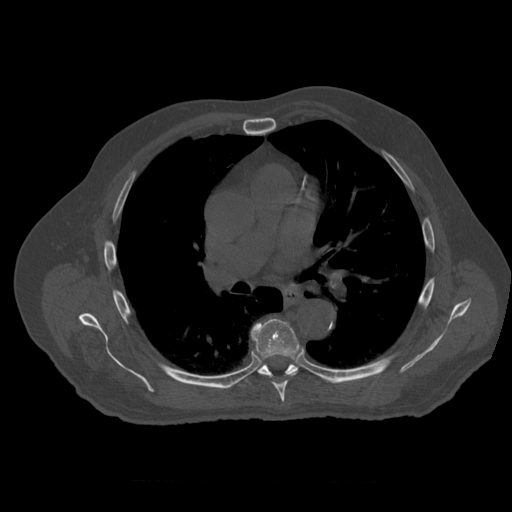
CT including the spine, one axial slice. Position 373 of 399 along the scan axis. Reconstruction kernel STANDARD. 120 kVp. Bone window (W 1800 / L 400 HU). 1.25 mm slice thickness. 512 × 512 image matrix, field of view 407 × 407 mm. Patient age 73 years. Case-level facts recorded for this patient, not image findings: primary cancer: prostate.
Structures marked on this image (semi-automatically segmented with operator editing):
- T6 vertebra: bounding box (x1, y1, x2, y2) in pixels: (251, 318, 300, 403)
- T7 vertebra: (242, 353, 320, 387)